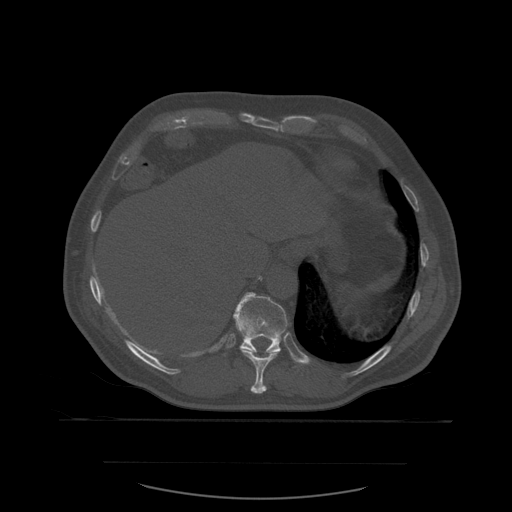
CT including the spine, one axial slice; slice 308 of 590 in the series (ordered by position); bone window (W 1800 / L 400 HU); 512 × 512 image matrix, field of view 479 × 479 mm. Patient age 71 years. Case-level facts recorded for this patient, not image findings: primary cancer: lung.
Outlined on this slice (semi-automatic segmentation, software-assisted and operator-edited):
- T10 vertebra: bounding box <236,325,282,394> (left, top, right, bottom; pixels)
- T11 vertebra: <233,292,288,355>